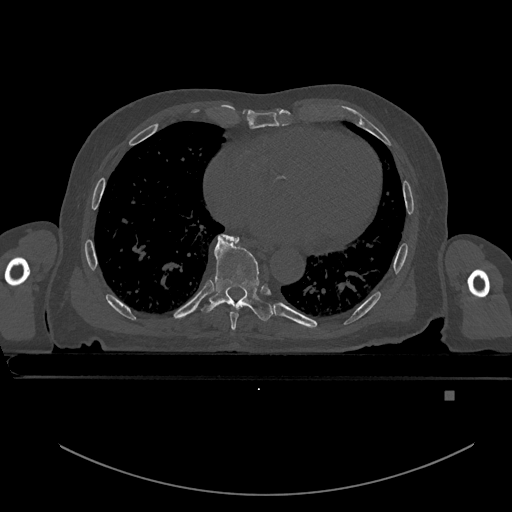
CT including the spine, one axial slice. Bone window (W 1800 / L 400 HU). 512 × 512 image matrix, field of view 456 × 456 mm. Patient: male, 82 years. From the clinical record (not read from this slice): primary cancer: prostate; vertebrae with lytic lesions (as recorded): T11, T9, T8, T2.
Annotated regions visible in this slice (semi-automatic segmentation, software-assisted and operator-edited):
- T7 vertebra: bounding box [x1, y1, x2, y2] px = [225, 235, 239, 329]
- T8 vertebra: [202, 234, 273, 321]